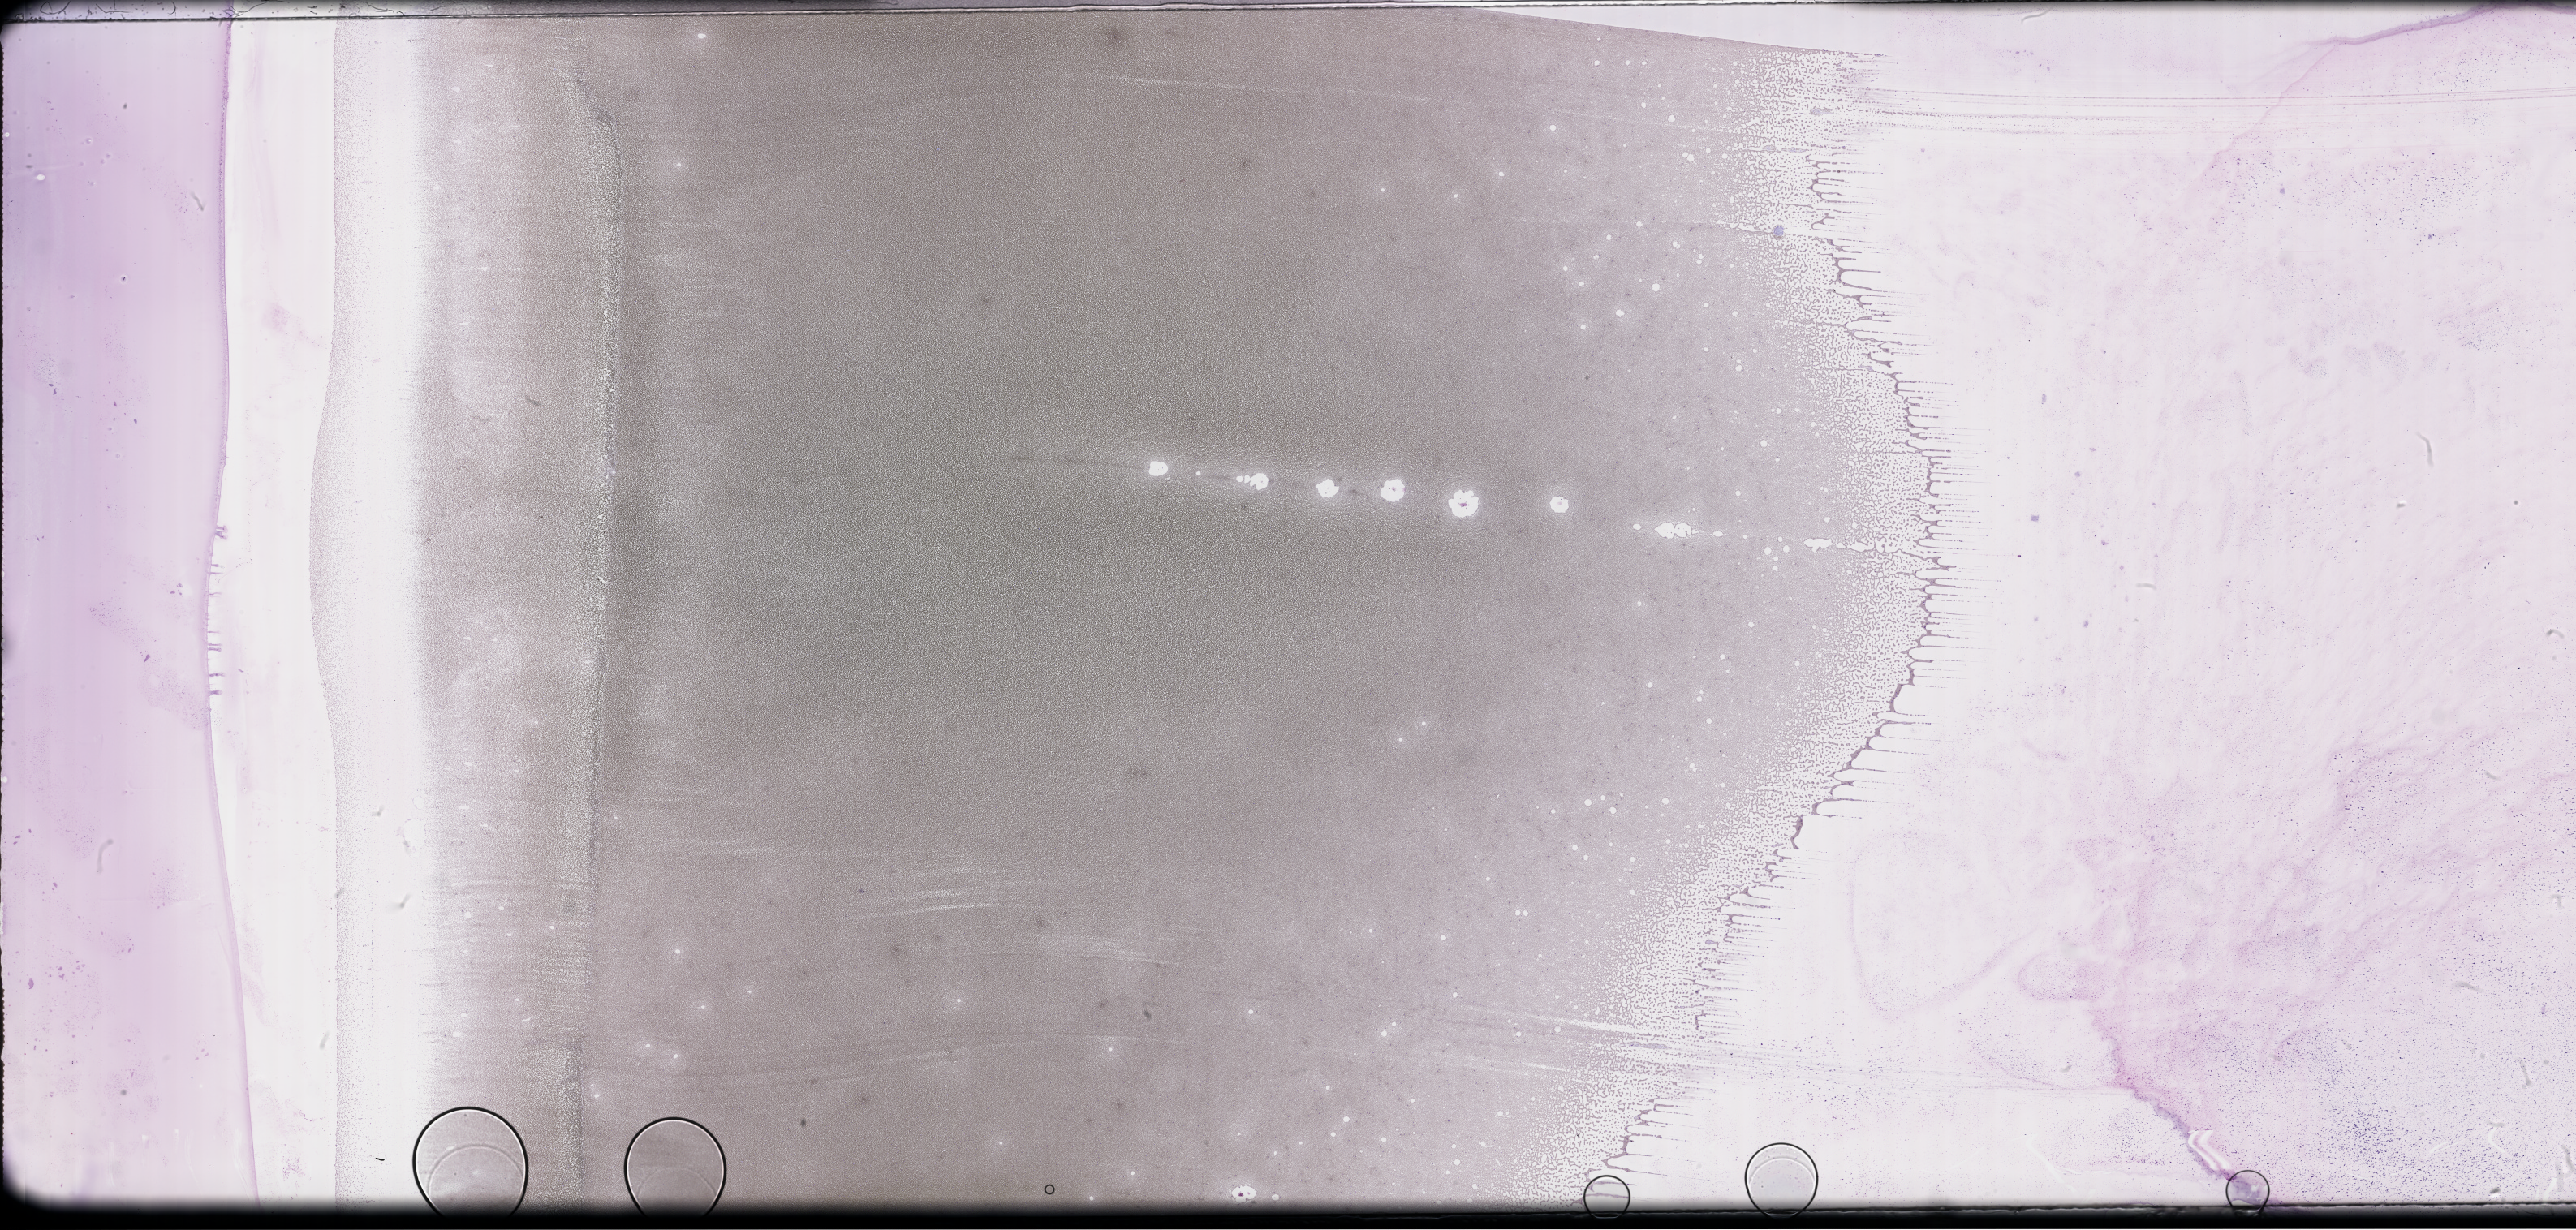
Wright-Giemsa-stained whole blood smear, whole-slide image, whole scanned area (about 51.3 x 24.5 mm) shown as a low-resolution overview, smear from an EDTA sample. Male patient.
* from a patient with: Plasma Cell Myeloma